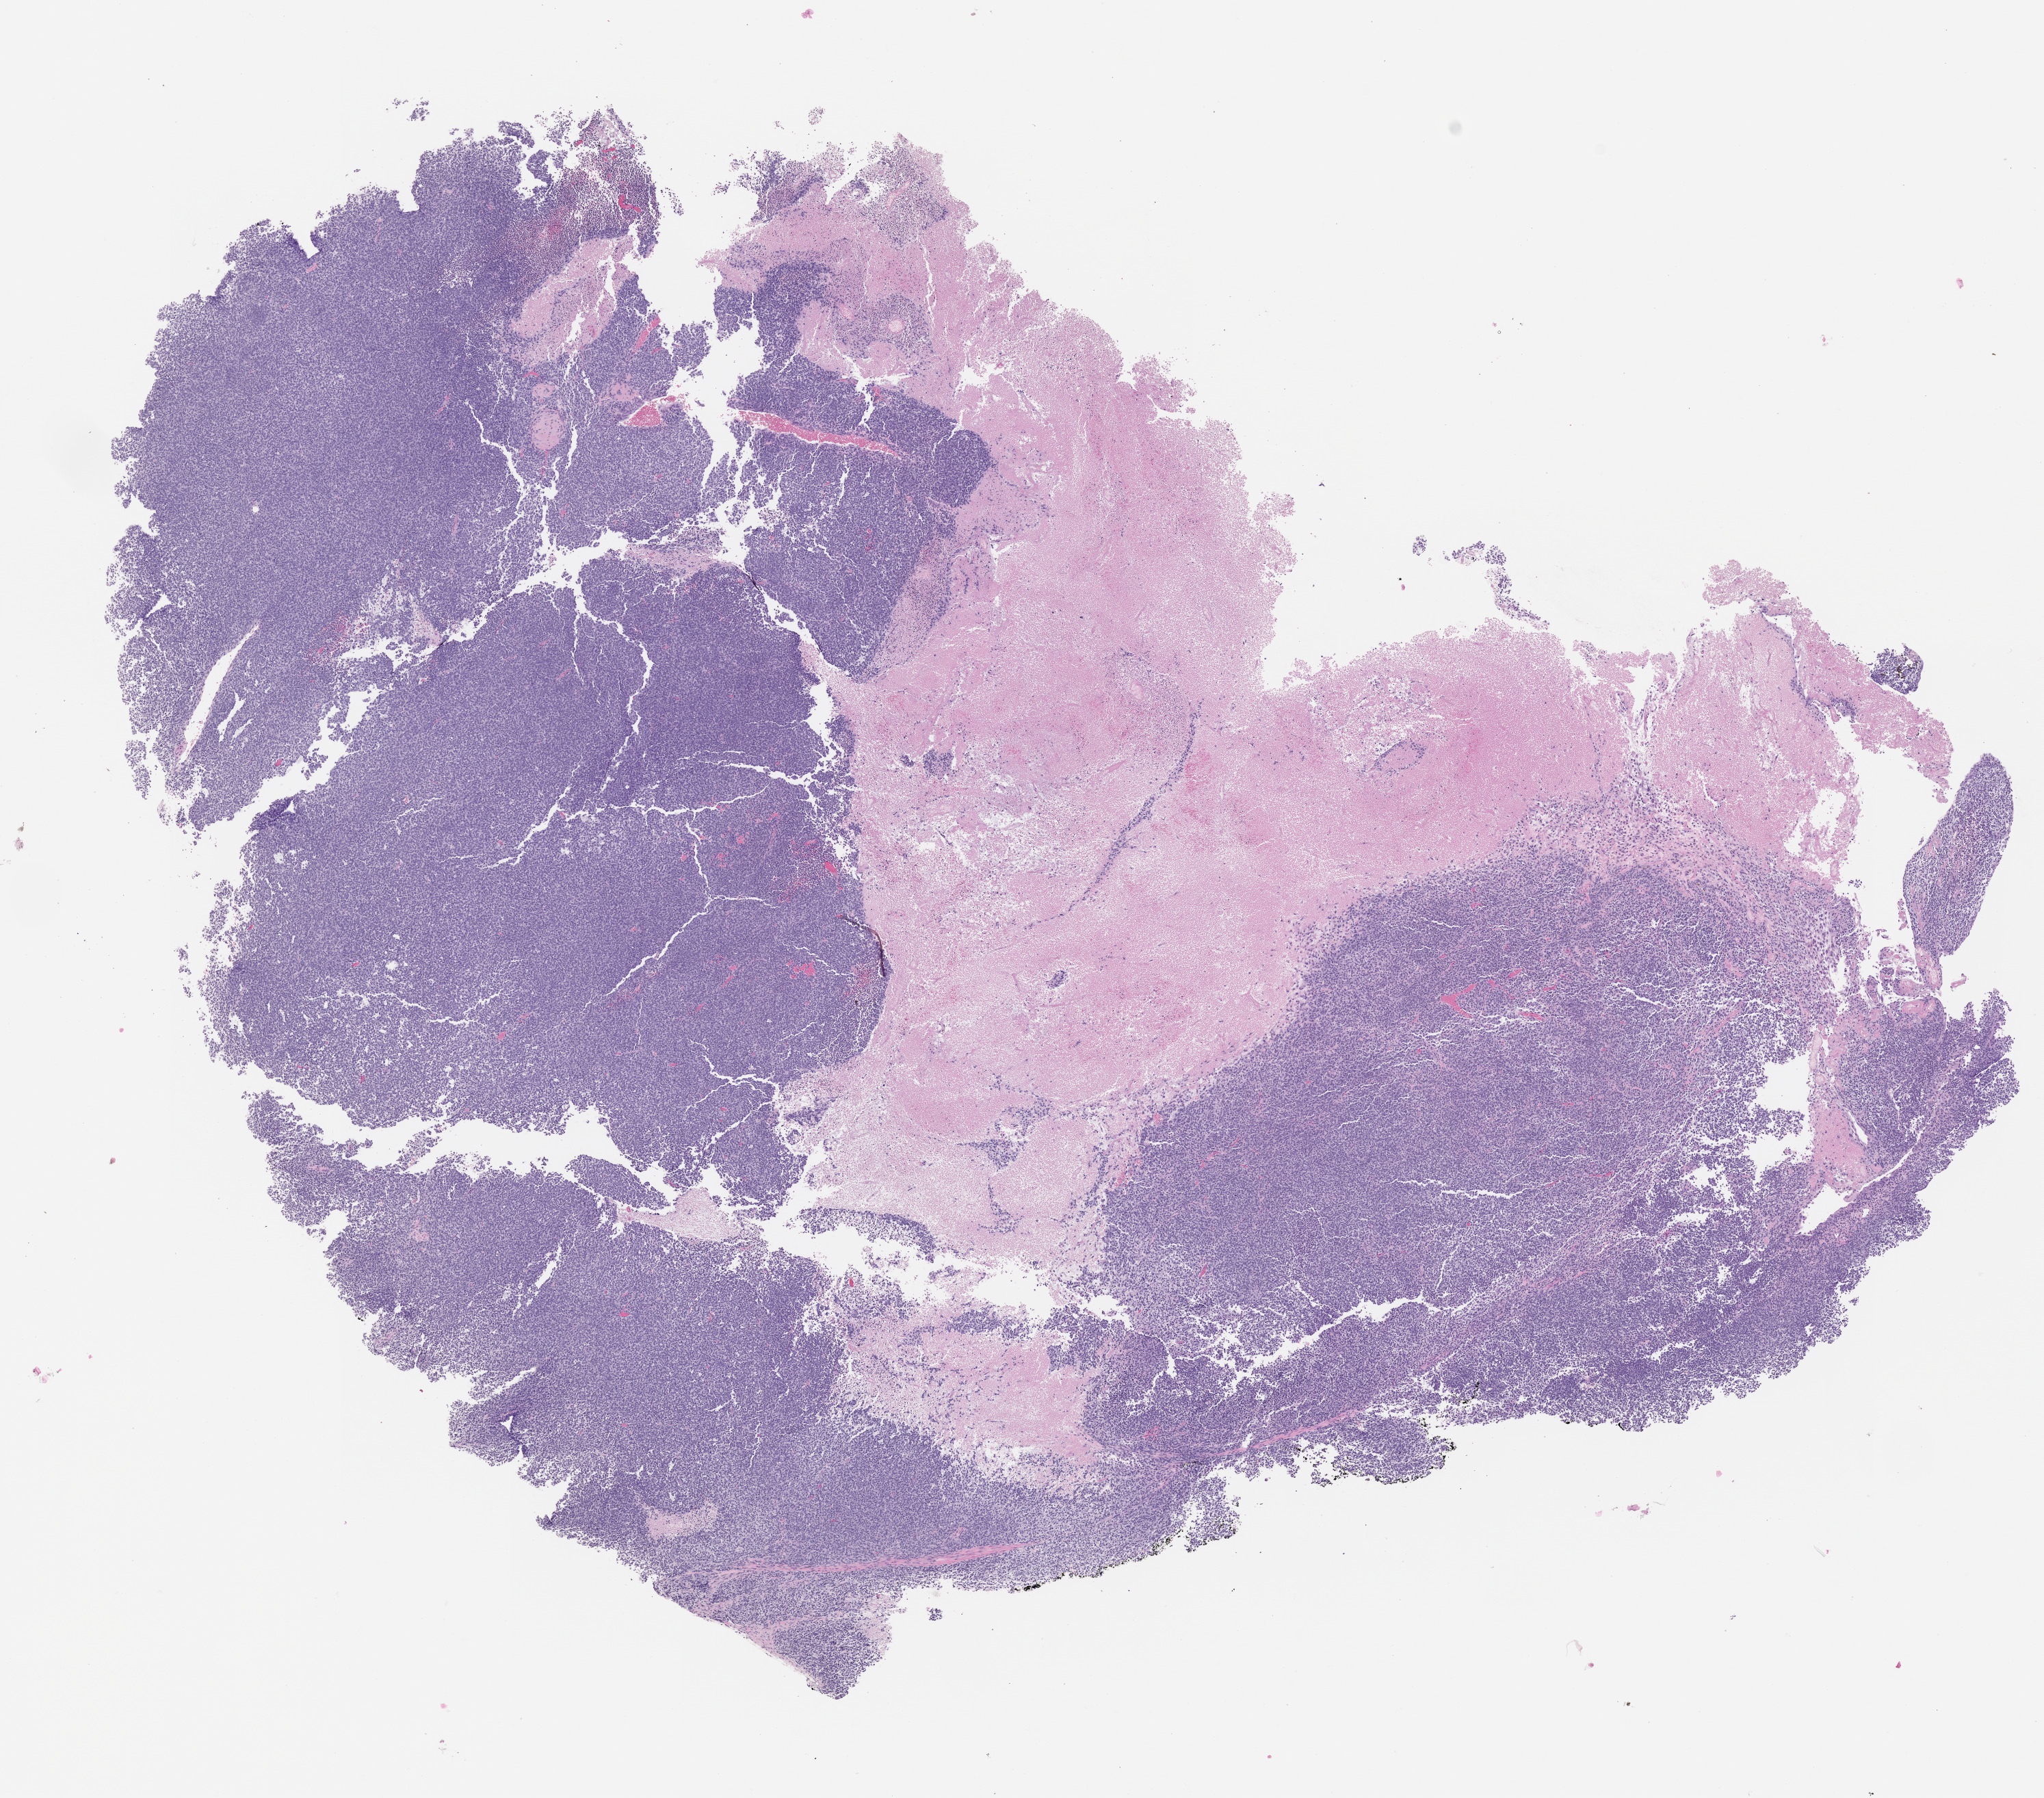
Hematoxylin and eosin (H&E) whole-slide image of a patient-derived xenograft (PDX) tumor grown in a mouse, passage 1 — shown as a low-resolution overview of the whole scanned area (about 12.0 x 10.6 mm). Formalin-fixed, paraffin-embedded (FFPE) tissue. Tumor site category: musculoskeletal.
• originating patient diagnosis: Ewing Sarcoma|Primitive Neuroectodermal Tumor